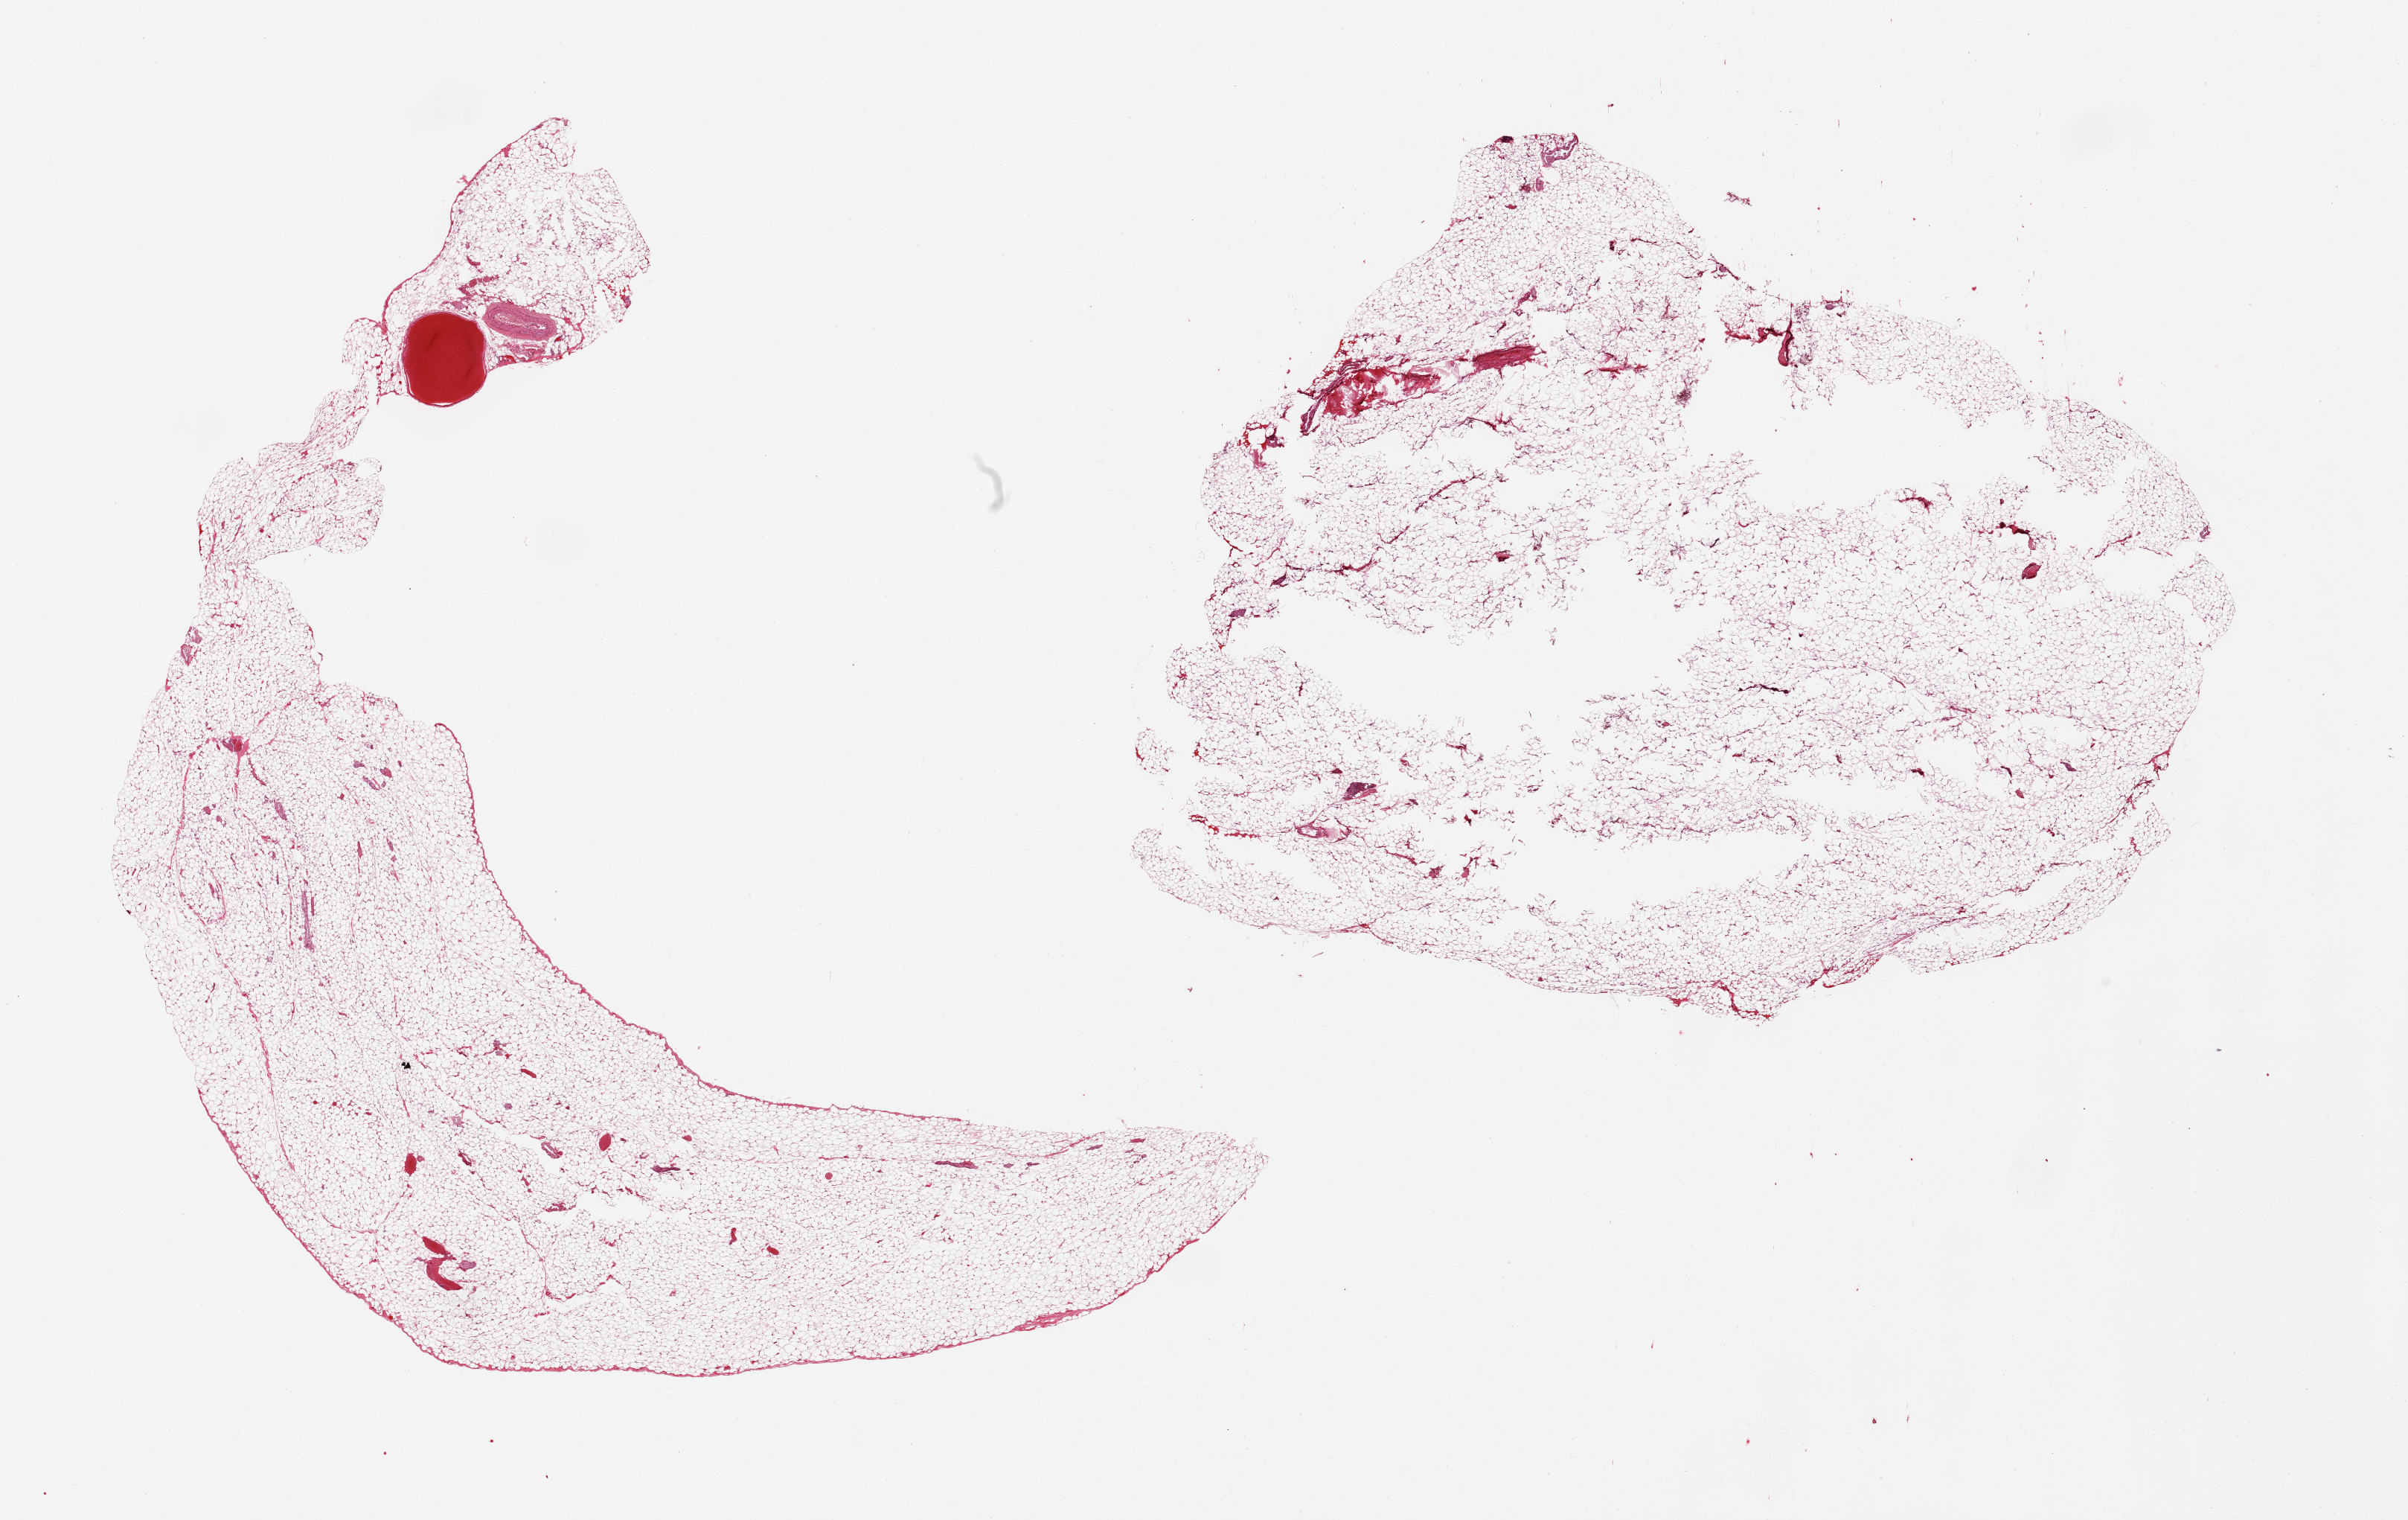
Hematoxylin and eosin (H&E) whole-slide image, brightfield — a low-resolution overview of the entire scanned area, about 25.6 x 16.2 mm (from a 20x scan); PAXgene-fixed paraffin-embedded (PFPE) section; section of omentum (target tissue); tissue donor sample. Male donor.
- review note (as recorded): 2 pieces no abnormalities